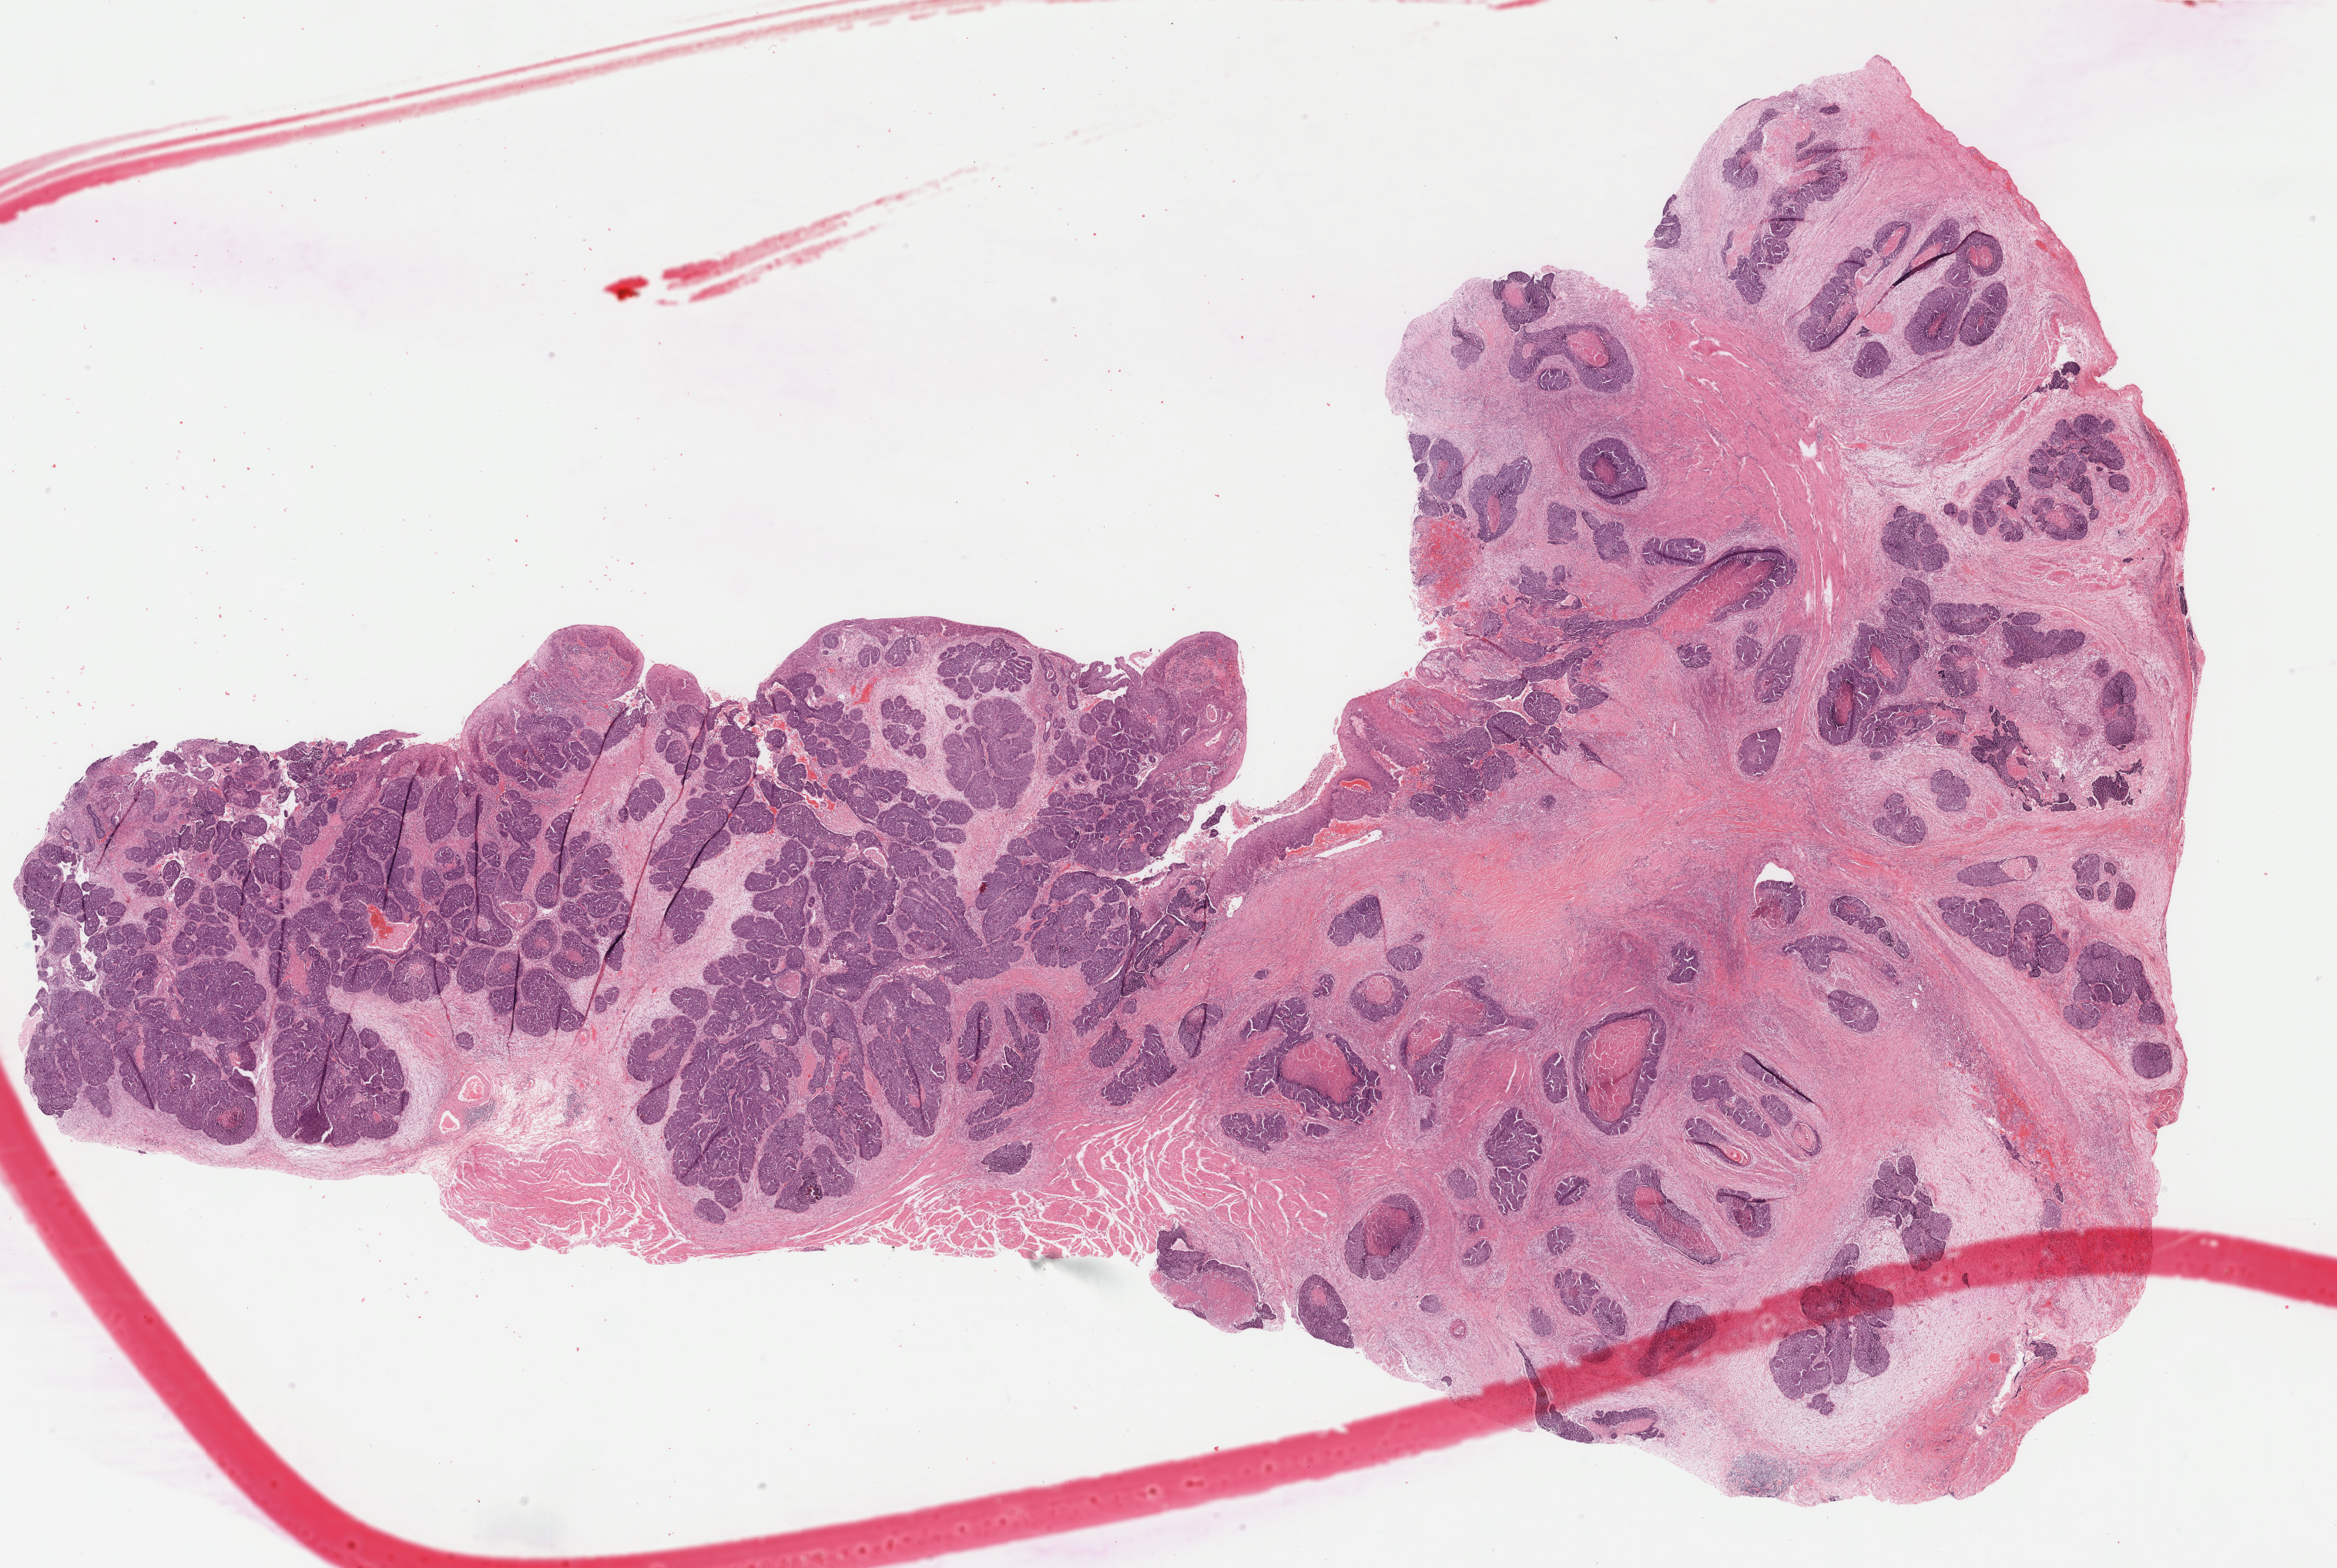
H&E-stained whole-slide image — shown as a low-resolution overview of the whole scanned area (about 24.1 x 16.2 mm, from a 40x scan), formalin-fixed paraffin-embedded (FFPE) diagnostic section, esophagus, primary tumour sample. Patient: female, age at initial diagnosis 51 years. Histologic grade: G2 (moderately differentiated).
Lymph nodes positive (case pathology): 0 of 5 examined. Pathologic diagnosis: Squamous cell carcinoma, keratinizing, NOS. AJCC pathologic stage: IIA (7th edition).